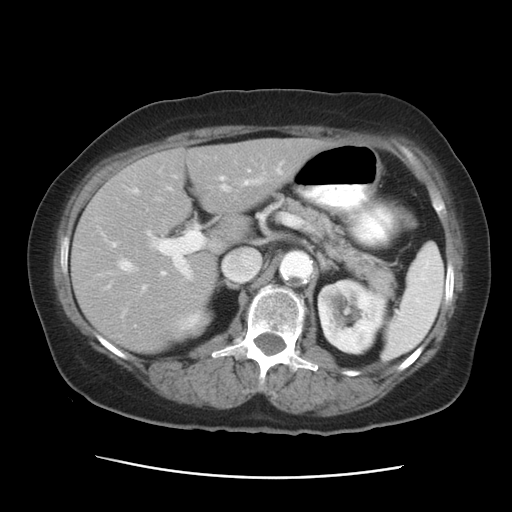
Contrast-enhanced abdominal CT, one axial slice. Position 17 of 29 along the scan axis. Reconstruction kernel STANDARD. 120 kVp. Intravenous contrast given. Soft-tissue window (W 400 / L 40 HU). 512 × 512 image matrix, field of view 354 × 354 mm. Female patient, age 64 years. Case-level facts recorded for this patient, not image findings: diagnosis: colorectal cancer liver metastases, imaged before liver resection; multiple liver metastases: no; largest metastasis: 2.5 cm; disease in both lobes: no.
Structures marked on this image (manually delineated by an expert):
- hepatic veins: bounding box [x1, y1, x2, y2] px = [117, 170, 281, 292]
- liver: [72, 138, 330, 352]
- planned liver remnant (the part of the liver to remain after resection): [72, 138, 331, 312]
- portal vein (with intrahepatic branches): [111, 176, 258, 280]